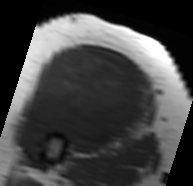
MRI of an extremity soft-tissue mass, one axial slice; slice 44 of 91 in the series (ordered by position); MR volume resampled by the dataset authors to the PET/CT grid (not the native acquisition matrix); 193 × 186 image matrix, field of view 188 × 182 mm. Female patient. Case-level facts recorded for this patient, not image findings: histological type: malignant solitary fibrous tumor; grade: intermediate; site of the primary tumour: right thigh.
Structures marked on this image (expert contour drawn on MRI and transferred to this co-registered scan by the dataset authors):
- gross tumour volume including surrounding oedema: bounding box [x1, y1, x2, y2] px = [22, 49, 151, 146]
- gross tumour volume (mass): [28, 49, 148, 145]